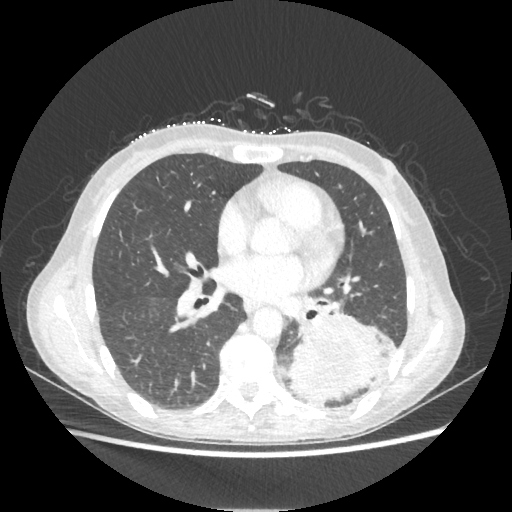
Chest CT, one axial slice. Slice 107 of 221 in the series (ordered by position). Reconstruction kernel STANDARD. Lung window (W 1500 / L -600 HU). 512 × 512 image matrix, field of view 360 × 360 mm. Female patient, age 53 years. Case-level facts recorded for this patient, not image findings: clinical TNM (as recorded): T3 N0 M0.
Structures marked on this image (bounding box drawn by a radiologist):
- lung tumour (recorded histology: adenocarcinoma): bounding box <289,313,390,404> (left, top, right, bottom; pixels)